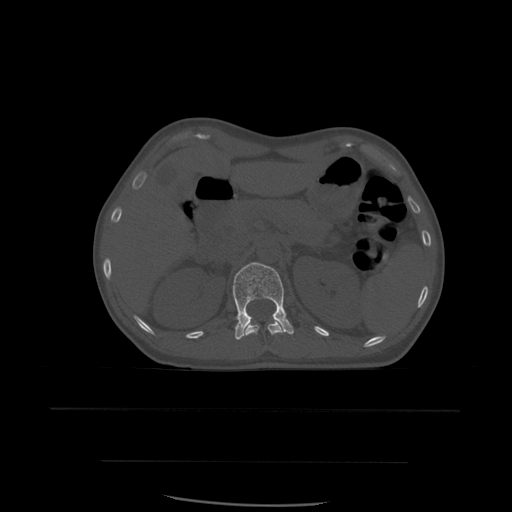
CT including the spine, one axial slice; position 257 of 574 along the scan axis; bone window (W 1800 / L 400 HU); 1.25 mm slice thickness; 512 × 512 image matrix, field of view 392 × 392 mm. Patient age 48 years. Case-level facts recorded for this patient, not image findings: primary cancer: lung.
Outlined on this slice (semi-automatically segmented with operator editing):
- L1 vertebra: bounding box (x1, y1, x2, y2) in pixels: (233, 263, 294, 340)
- T12 vertebra: (245, 319, 284, 336)